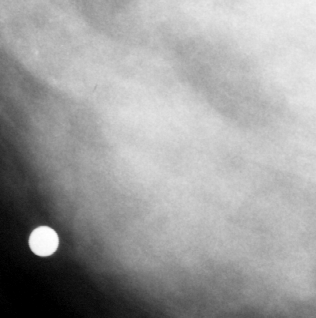
Crop from a digitized film mammogram around one marked abnormality, right breast, MLO view, BI-RADS breast density category 2 (scale 1–4).
Mass, shape oval, margins obscured; BI-RADS assessment category 4; pathology result (as recorded, not read from the image): malignant.